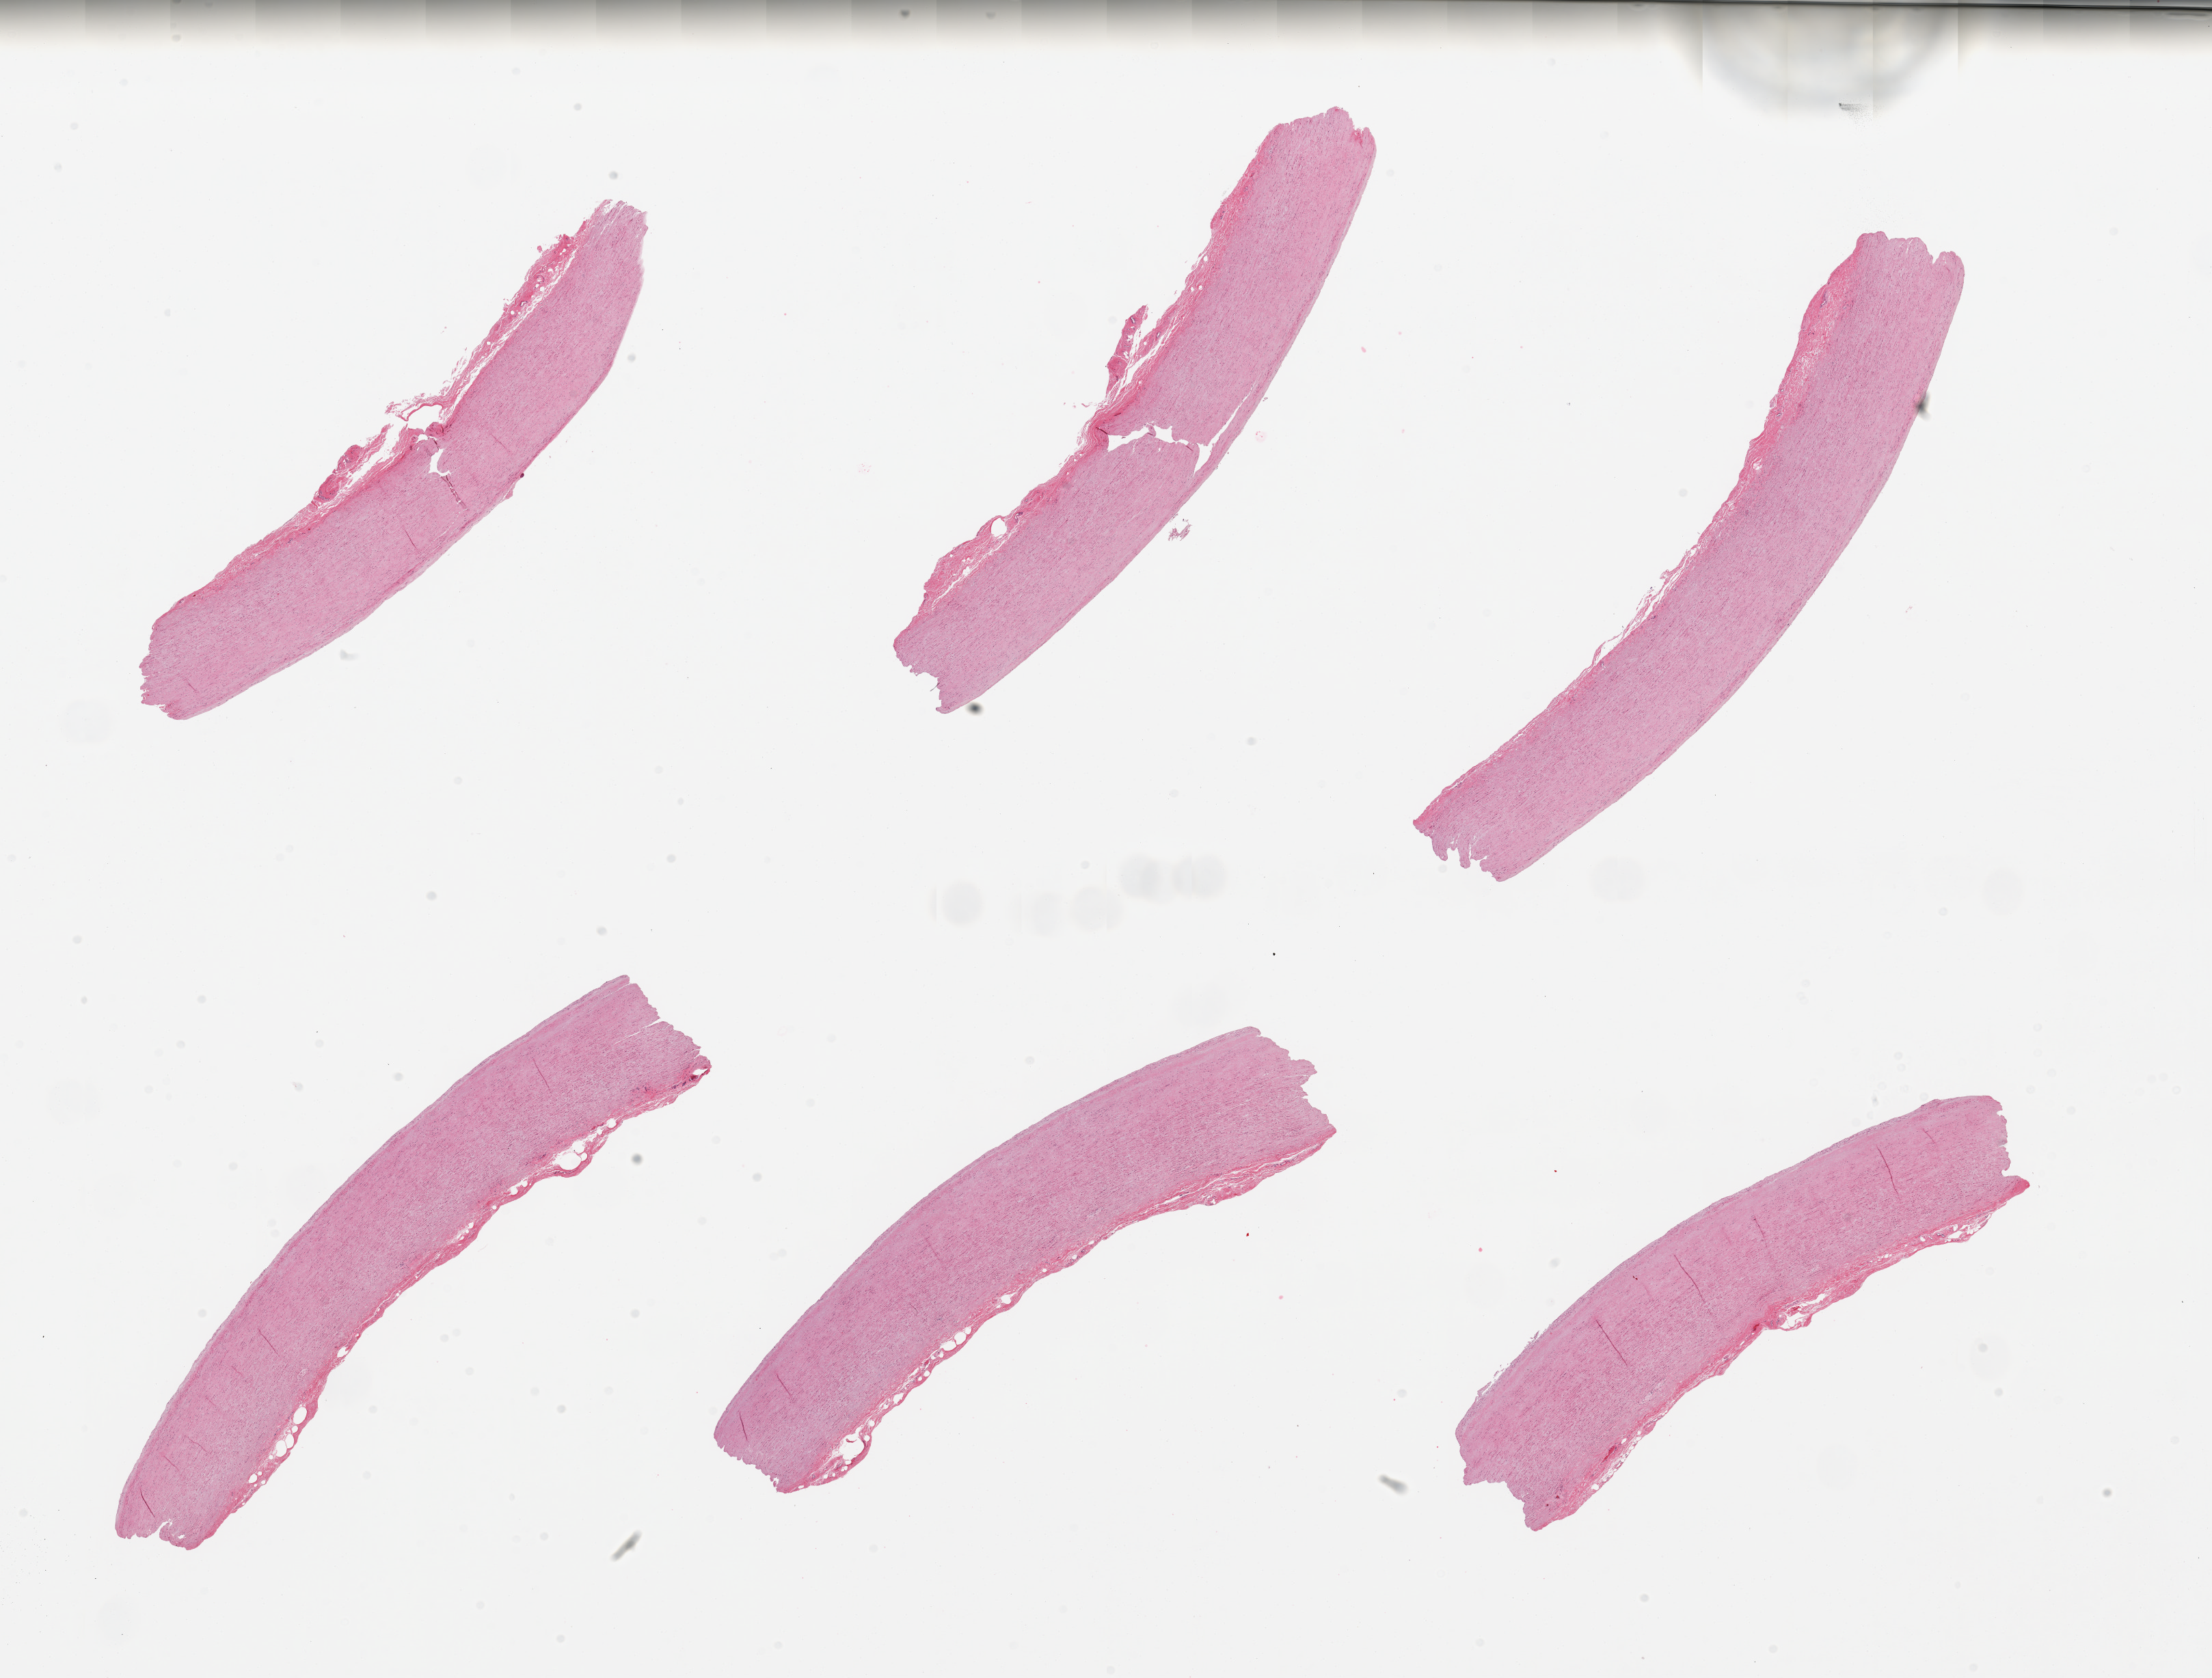
Digitized H&E-stained section, shown as a low-resolution overview of the whole scanned area (about 25.6 x 19.4 mm, acquisition: 20x scan). PAXgene-fixed, paraffin-embedded tissue. Target tissue: aorta. Donor tissue sample. Donor: male.
- pathologist's review note for this sample: 6 pieces, minimal atherosis